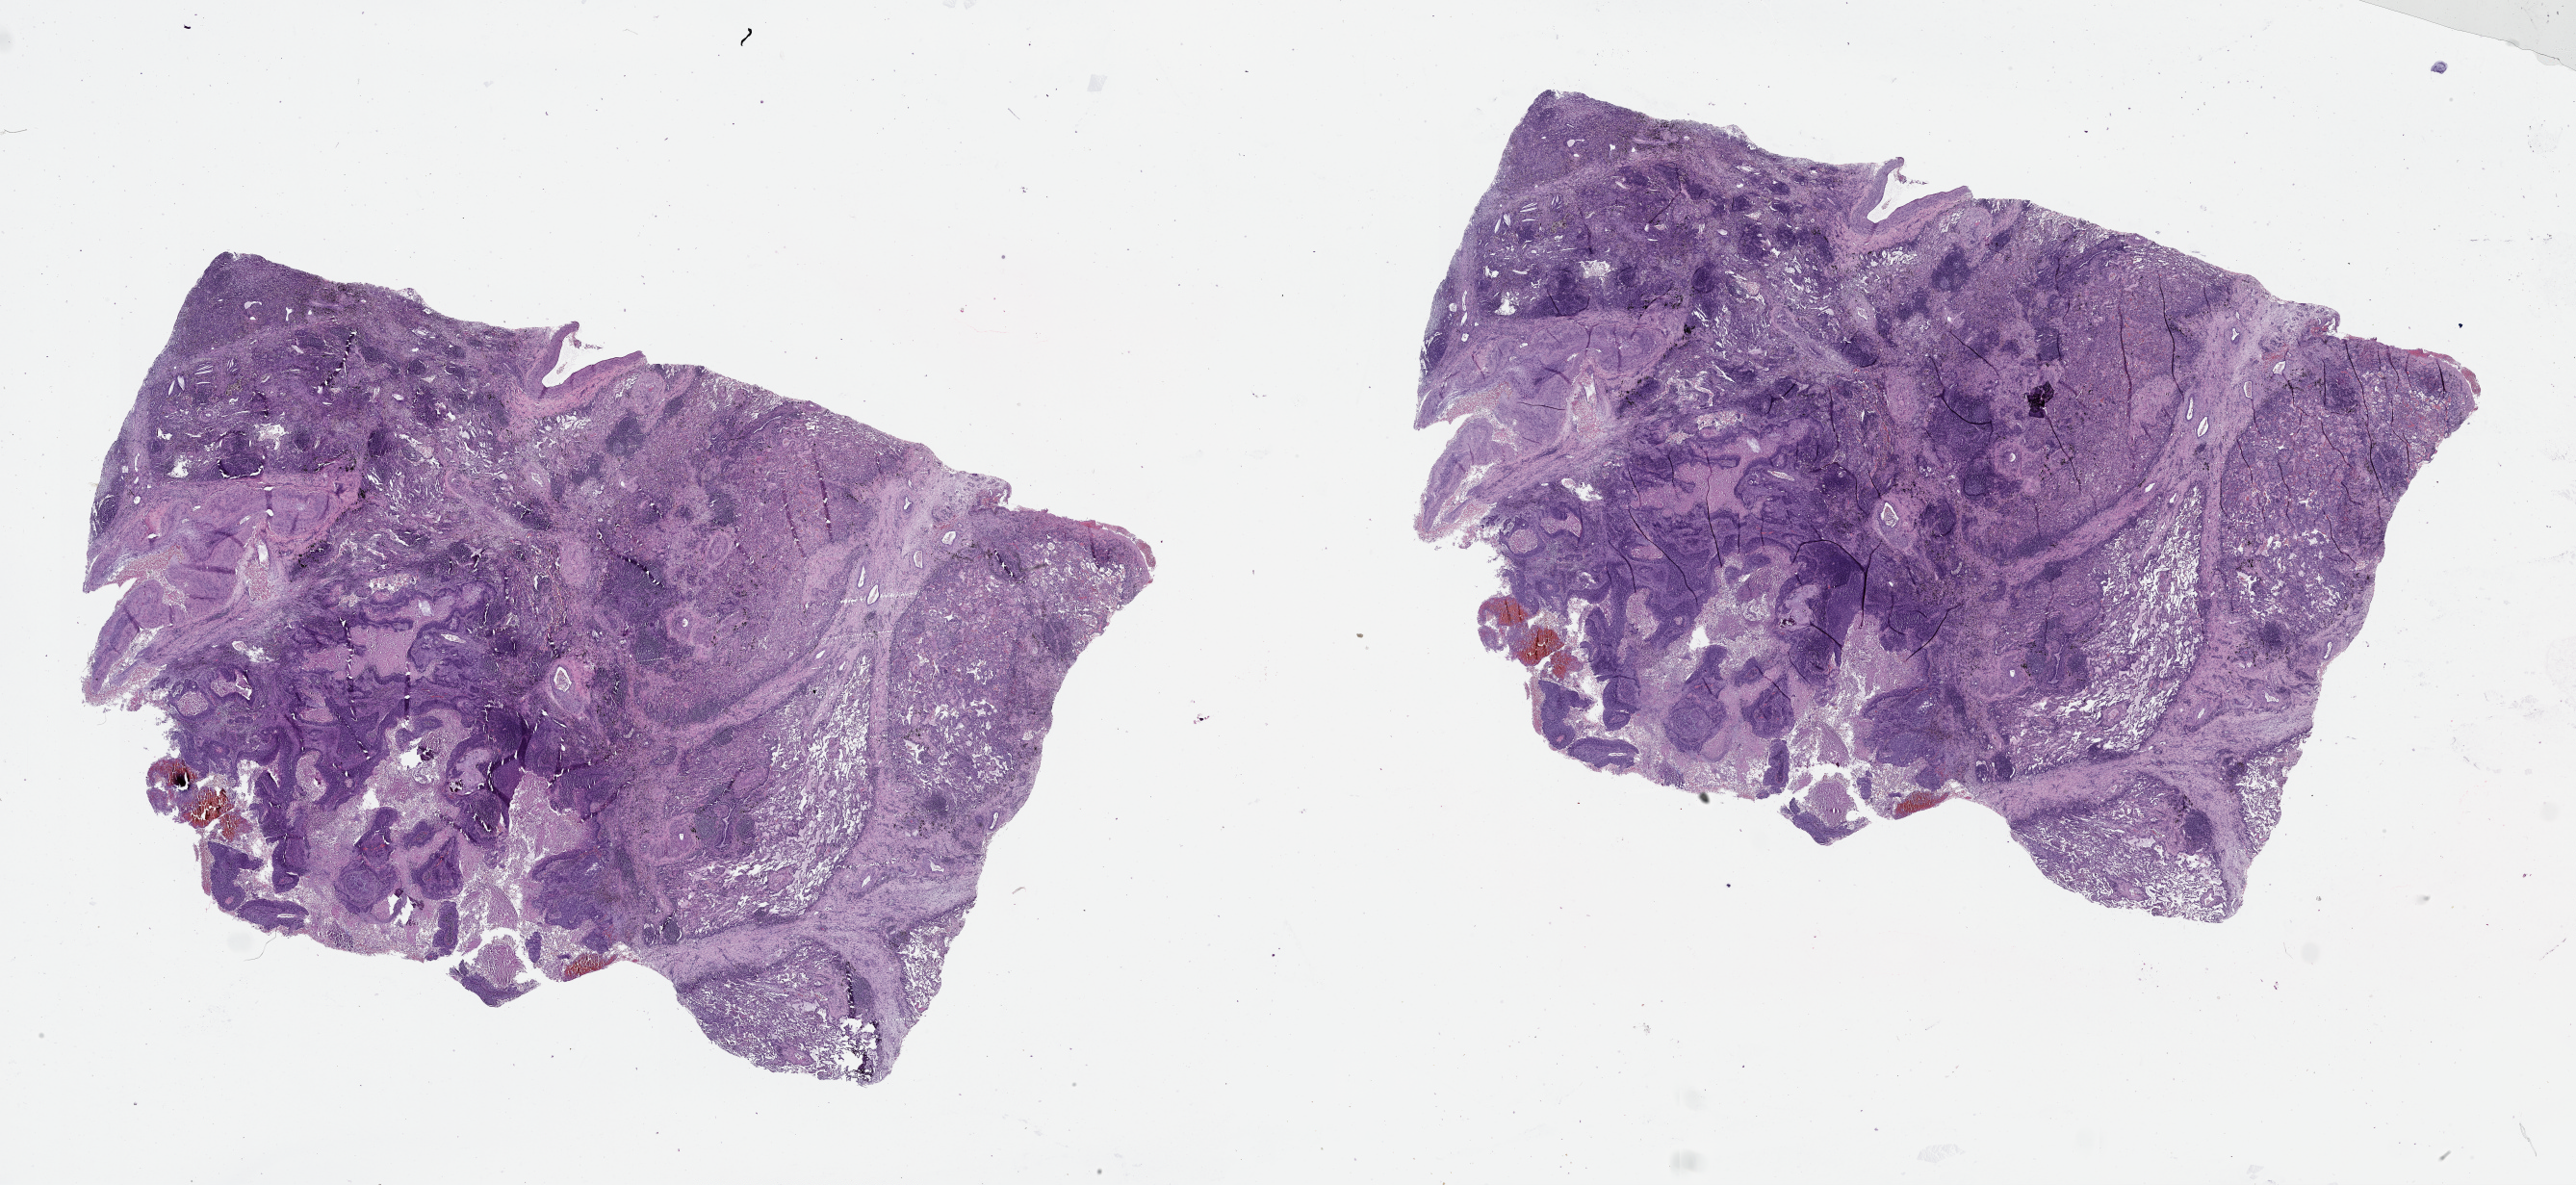
Whole-slide histology image, H&E, a low-resolution overview of the entire scanned area, about 43.1 x 19.8 mm (from a 20x scan); tumour tissue sample, lung. Patient: male, age 57 years.
Patient diagnosis (cohort enrolment): squamous cell carcinoma (lung).